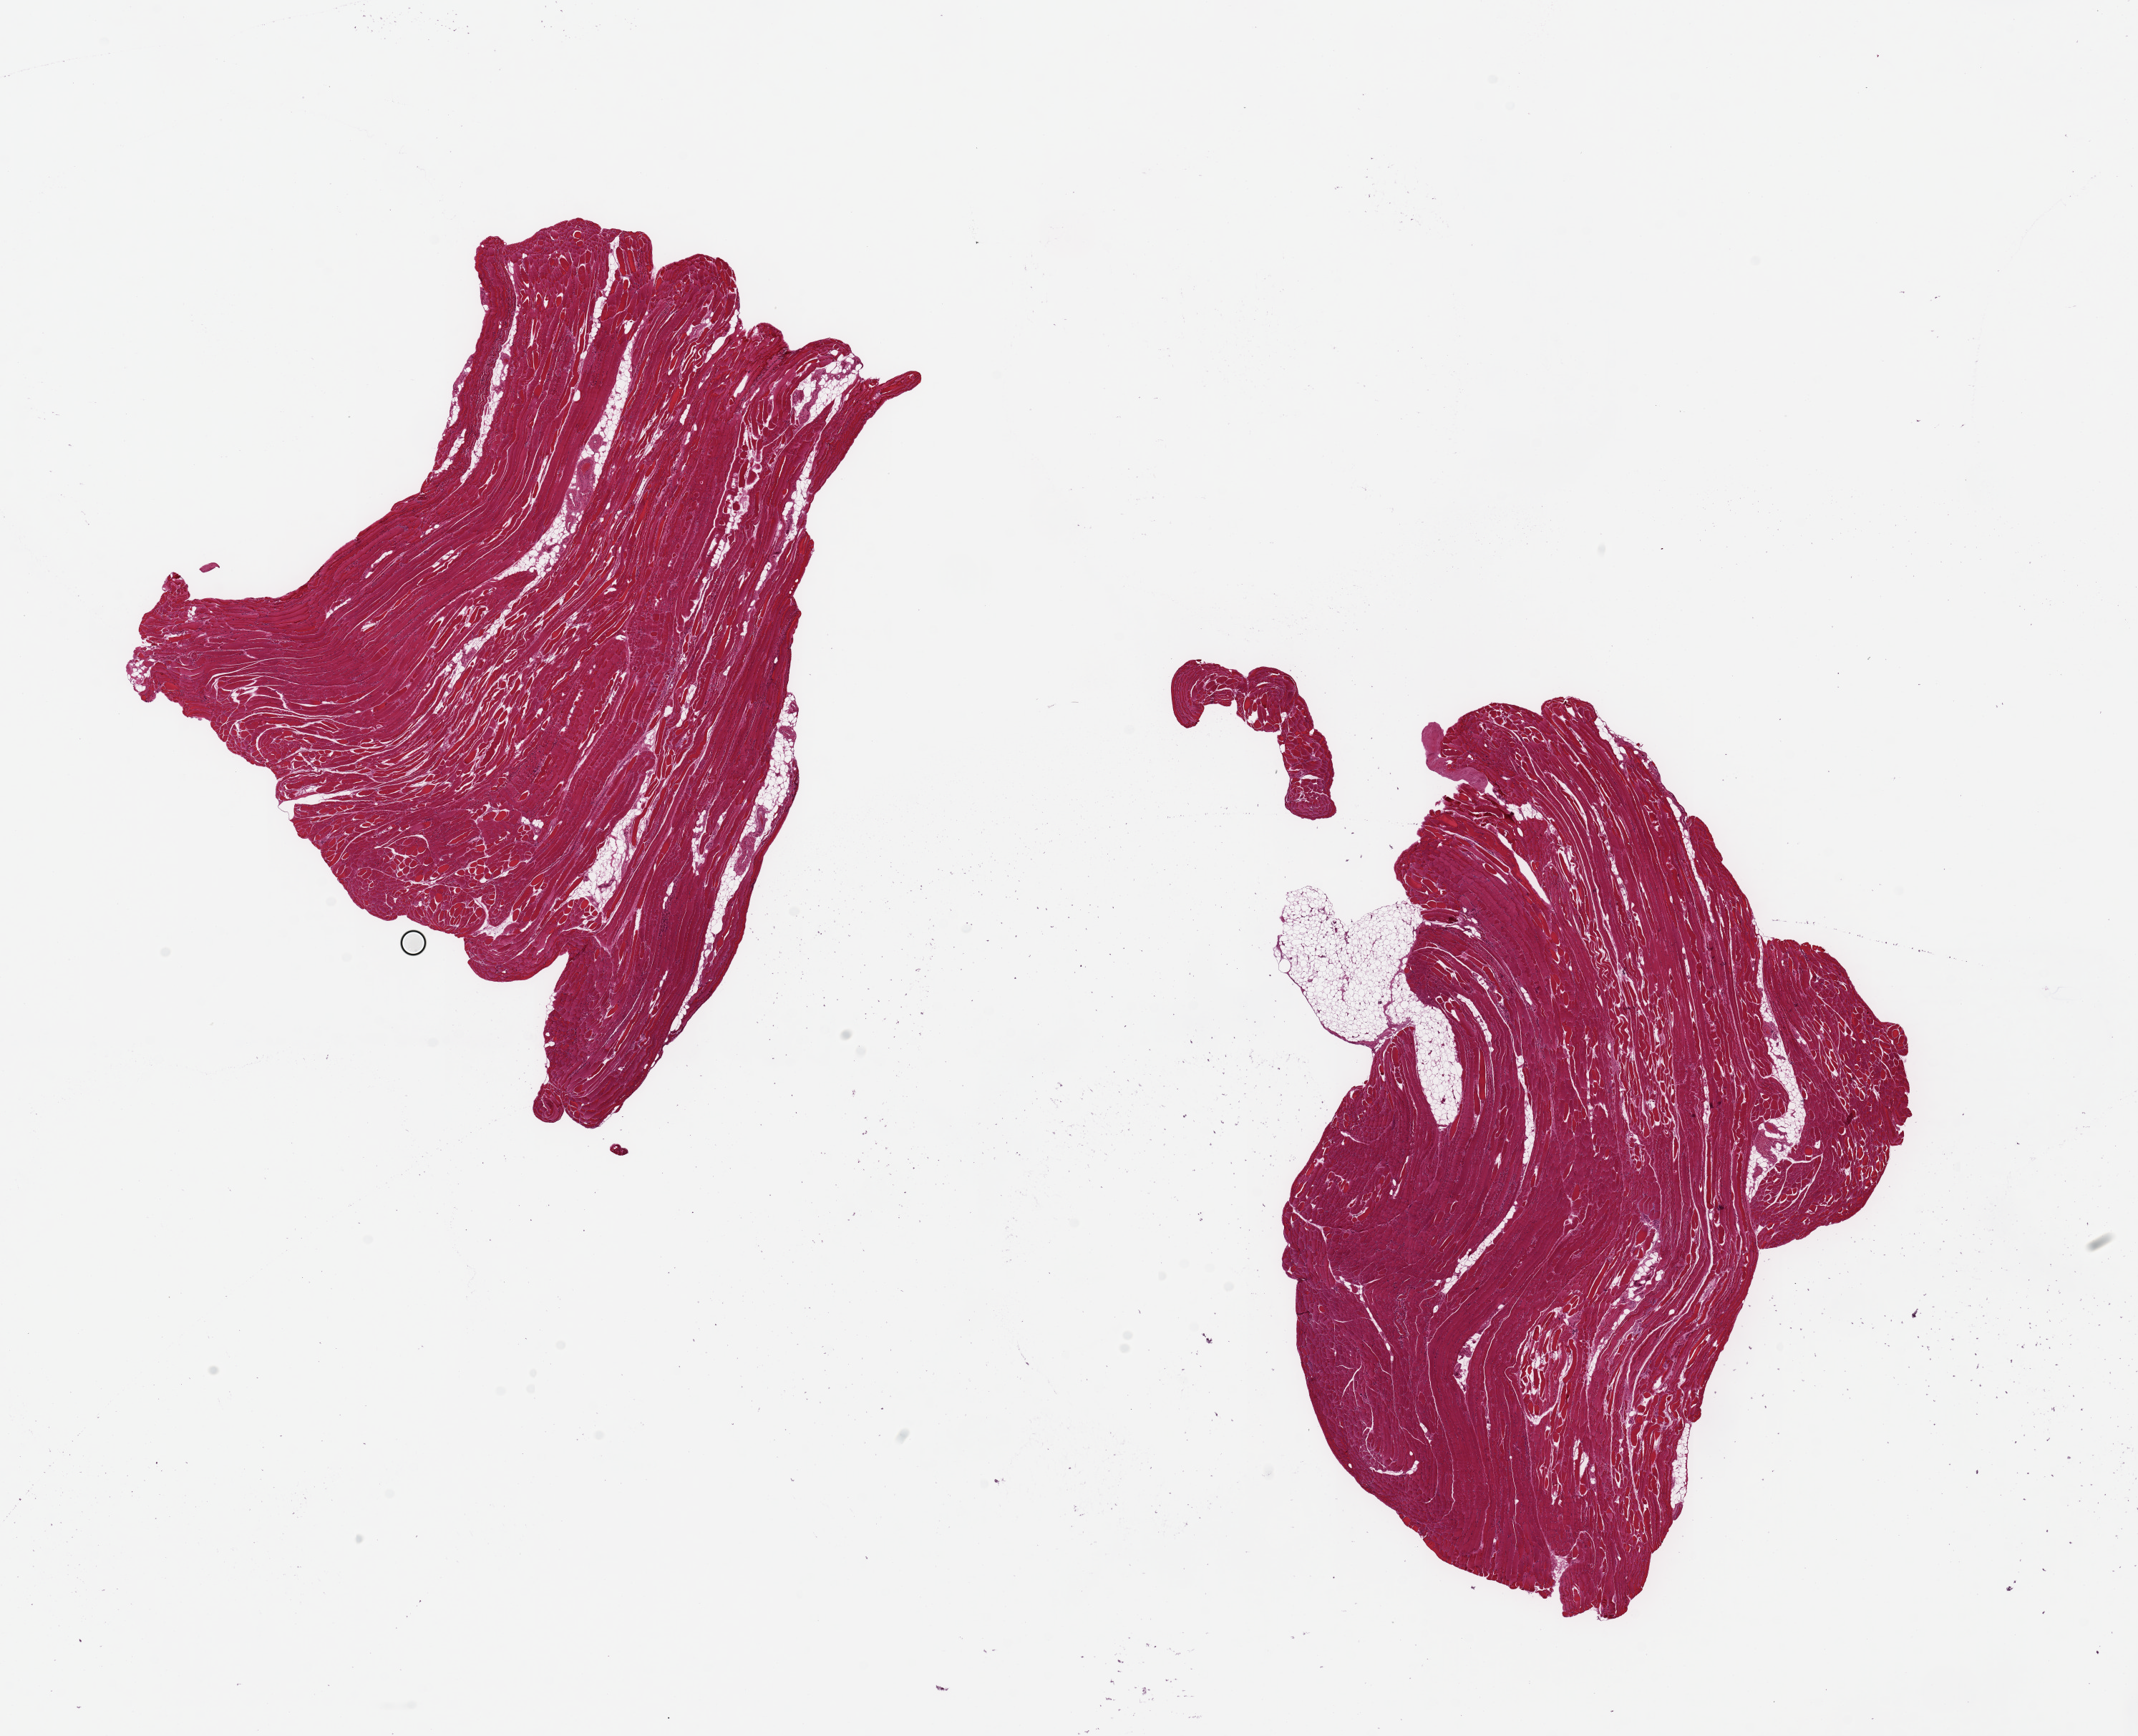
Digitized H&E-stained section, brightfield — low-resolution overview of the scanned area, about 23.6 x 19.2 mm, PAXgene-fixed paraffin-embedded (PFPE) section, sampled site (target tissue): skeletal muscle, tissue donor sample. Donor: male.
Pathologist's review note for this sample: 2 pieces, 9x8 & 10x9mm.